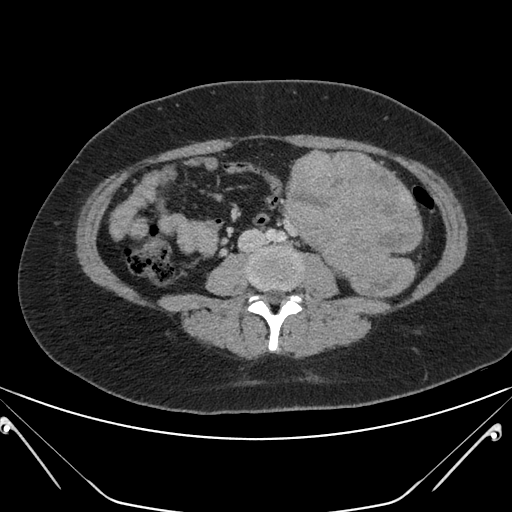
Contrast-enhanced abdominal CT, one axial slice; position 85 of 168 along the scan axis; soft-tissue window (W 400 / L 40 HU); 512 × 512 image matrix. Patient: female, 26 years. From the clinical record (not read from this slice): diagnosis: adrenocortical carcinoma; tumour side: left adrenal; tumour size at pathology: 28 cm; Ki-67 index: 20 %; stage (as recorded): 2.
Outlined on this slice (semi-automatically segmented with operator editing):
- mass: bounding box [x1, y1, x2, y2] px = [284, 150, 421, 294]